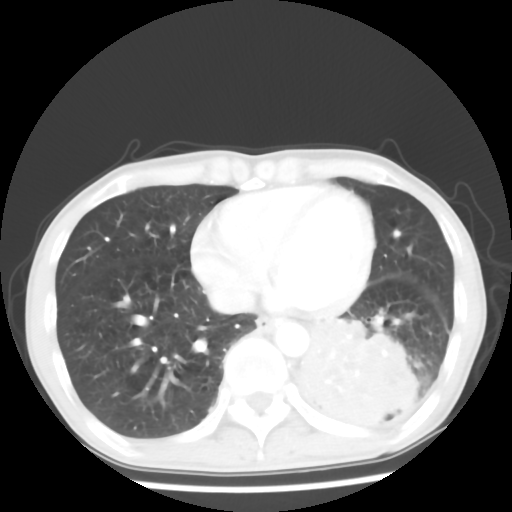
Chest CT, one axial slice; slice 21 of 64 in the series (ordered by position); lung window (W 1500 / L -600 HU); 5 mm slice thickness; 512 × 512 image matrix, field of view 313 × 313 mm. Patient: male, 68 years. Case-level facts recorded for this patient, not image findings: clinical TNM (as recorded): T4 N0 M0.
Structures marked on this image (rectangle marked by the reading radiologist):
- lung tumour (recorded histology: squamous cell carcinoma): bounding box (x1, y1, x2, y2) in pixels: (284, 305, 437, 445)